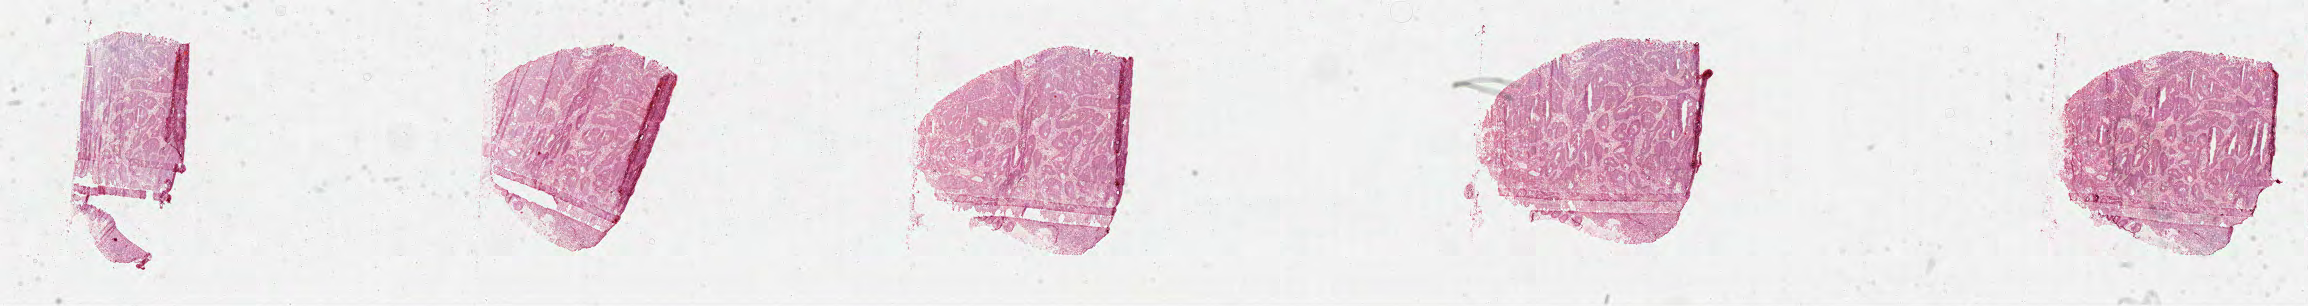
Whole-slide histology image, Hematoxylin and eosin (H&E) stained — low-resolution overview of the scanned area, about 37.2 x 4.9 mm (slide scanned at 40x), formalin-fixed paraffin-embedded (FFPE) diagnostic section, primary tumour sample from the colon. Female patient; age at initial diagnosis 76 years.
AJCC pathologic stage: IIA (7th edition). Histologic diagnosis: Adenocarcinoma, NOS (sigmoid colon). Lymph nodes positive (case pathology): 0 of 5 examined. TNM: T3 N0 M0.